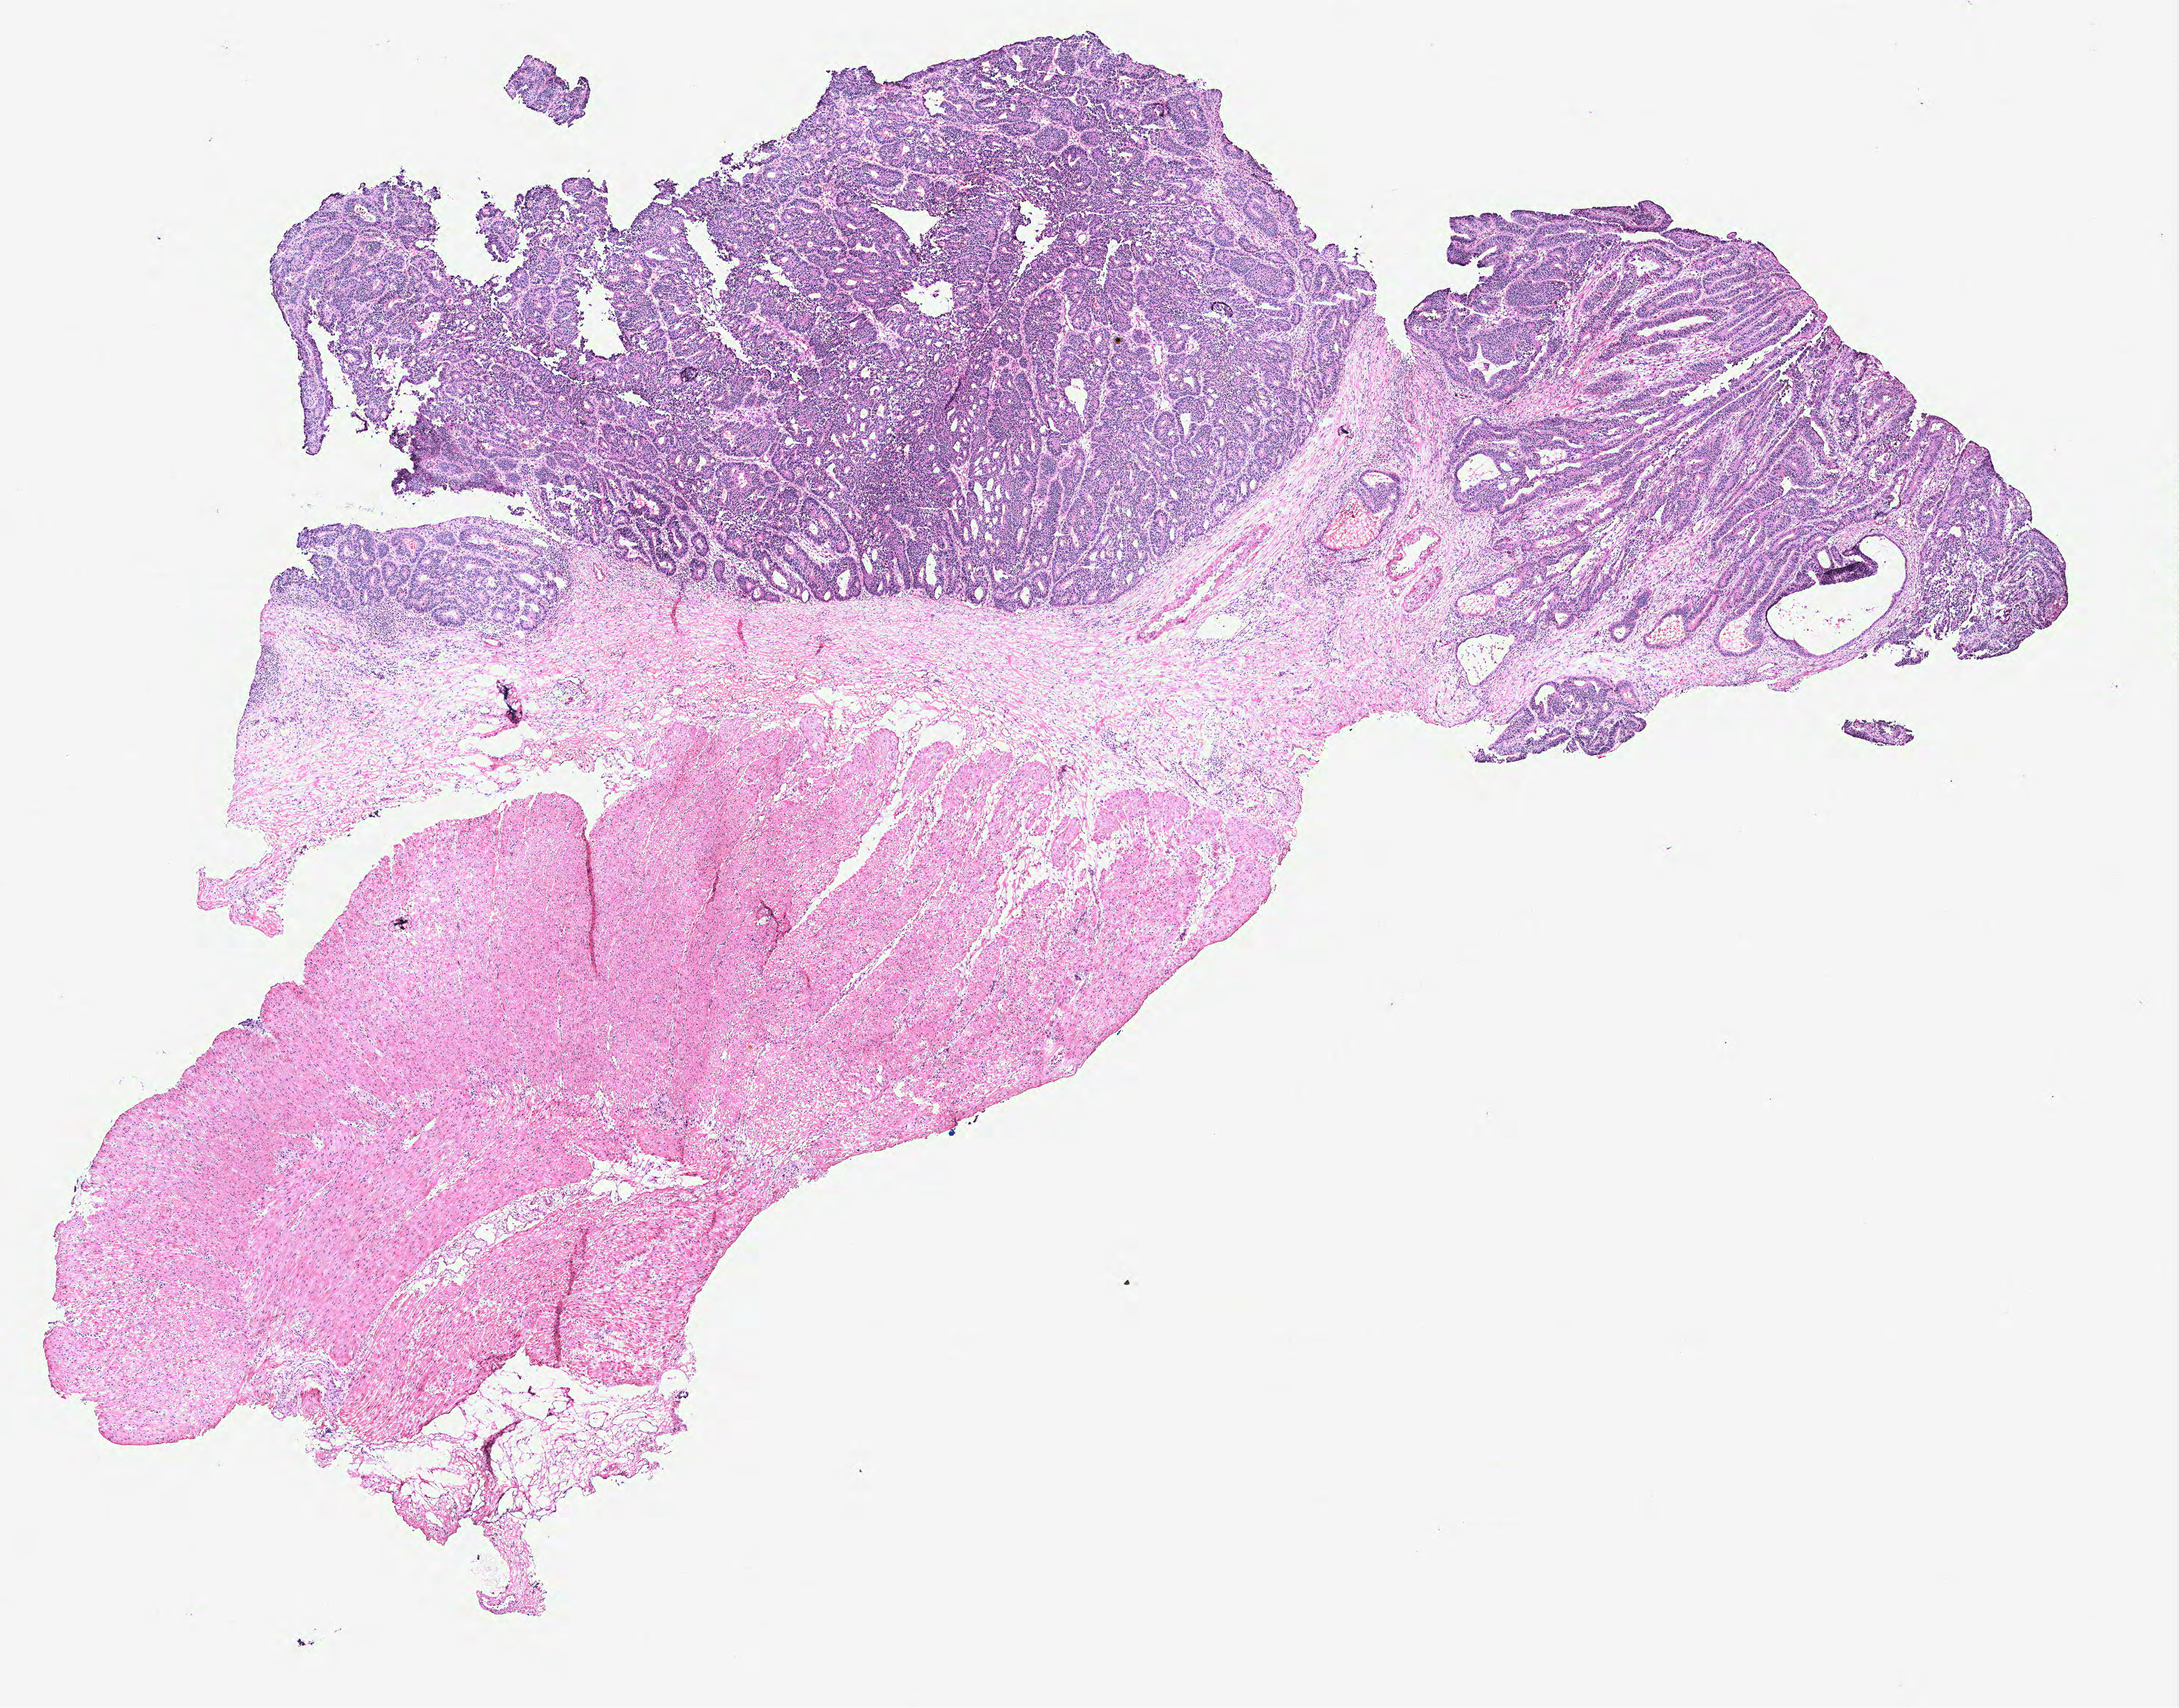
H&E-stained whole-slide image, a low-resolution overview of the entire scanned area, about 11.8 x 9.2 mm (slide scanned at 40x), colon, tissue type not recorded.
Patient diagnosis (cohort enrolment): colon cancer (colon).